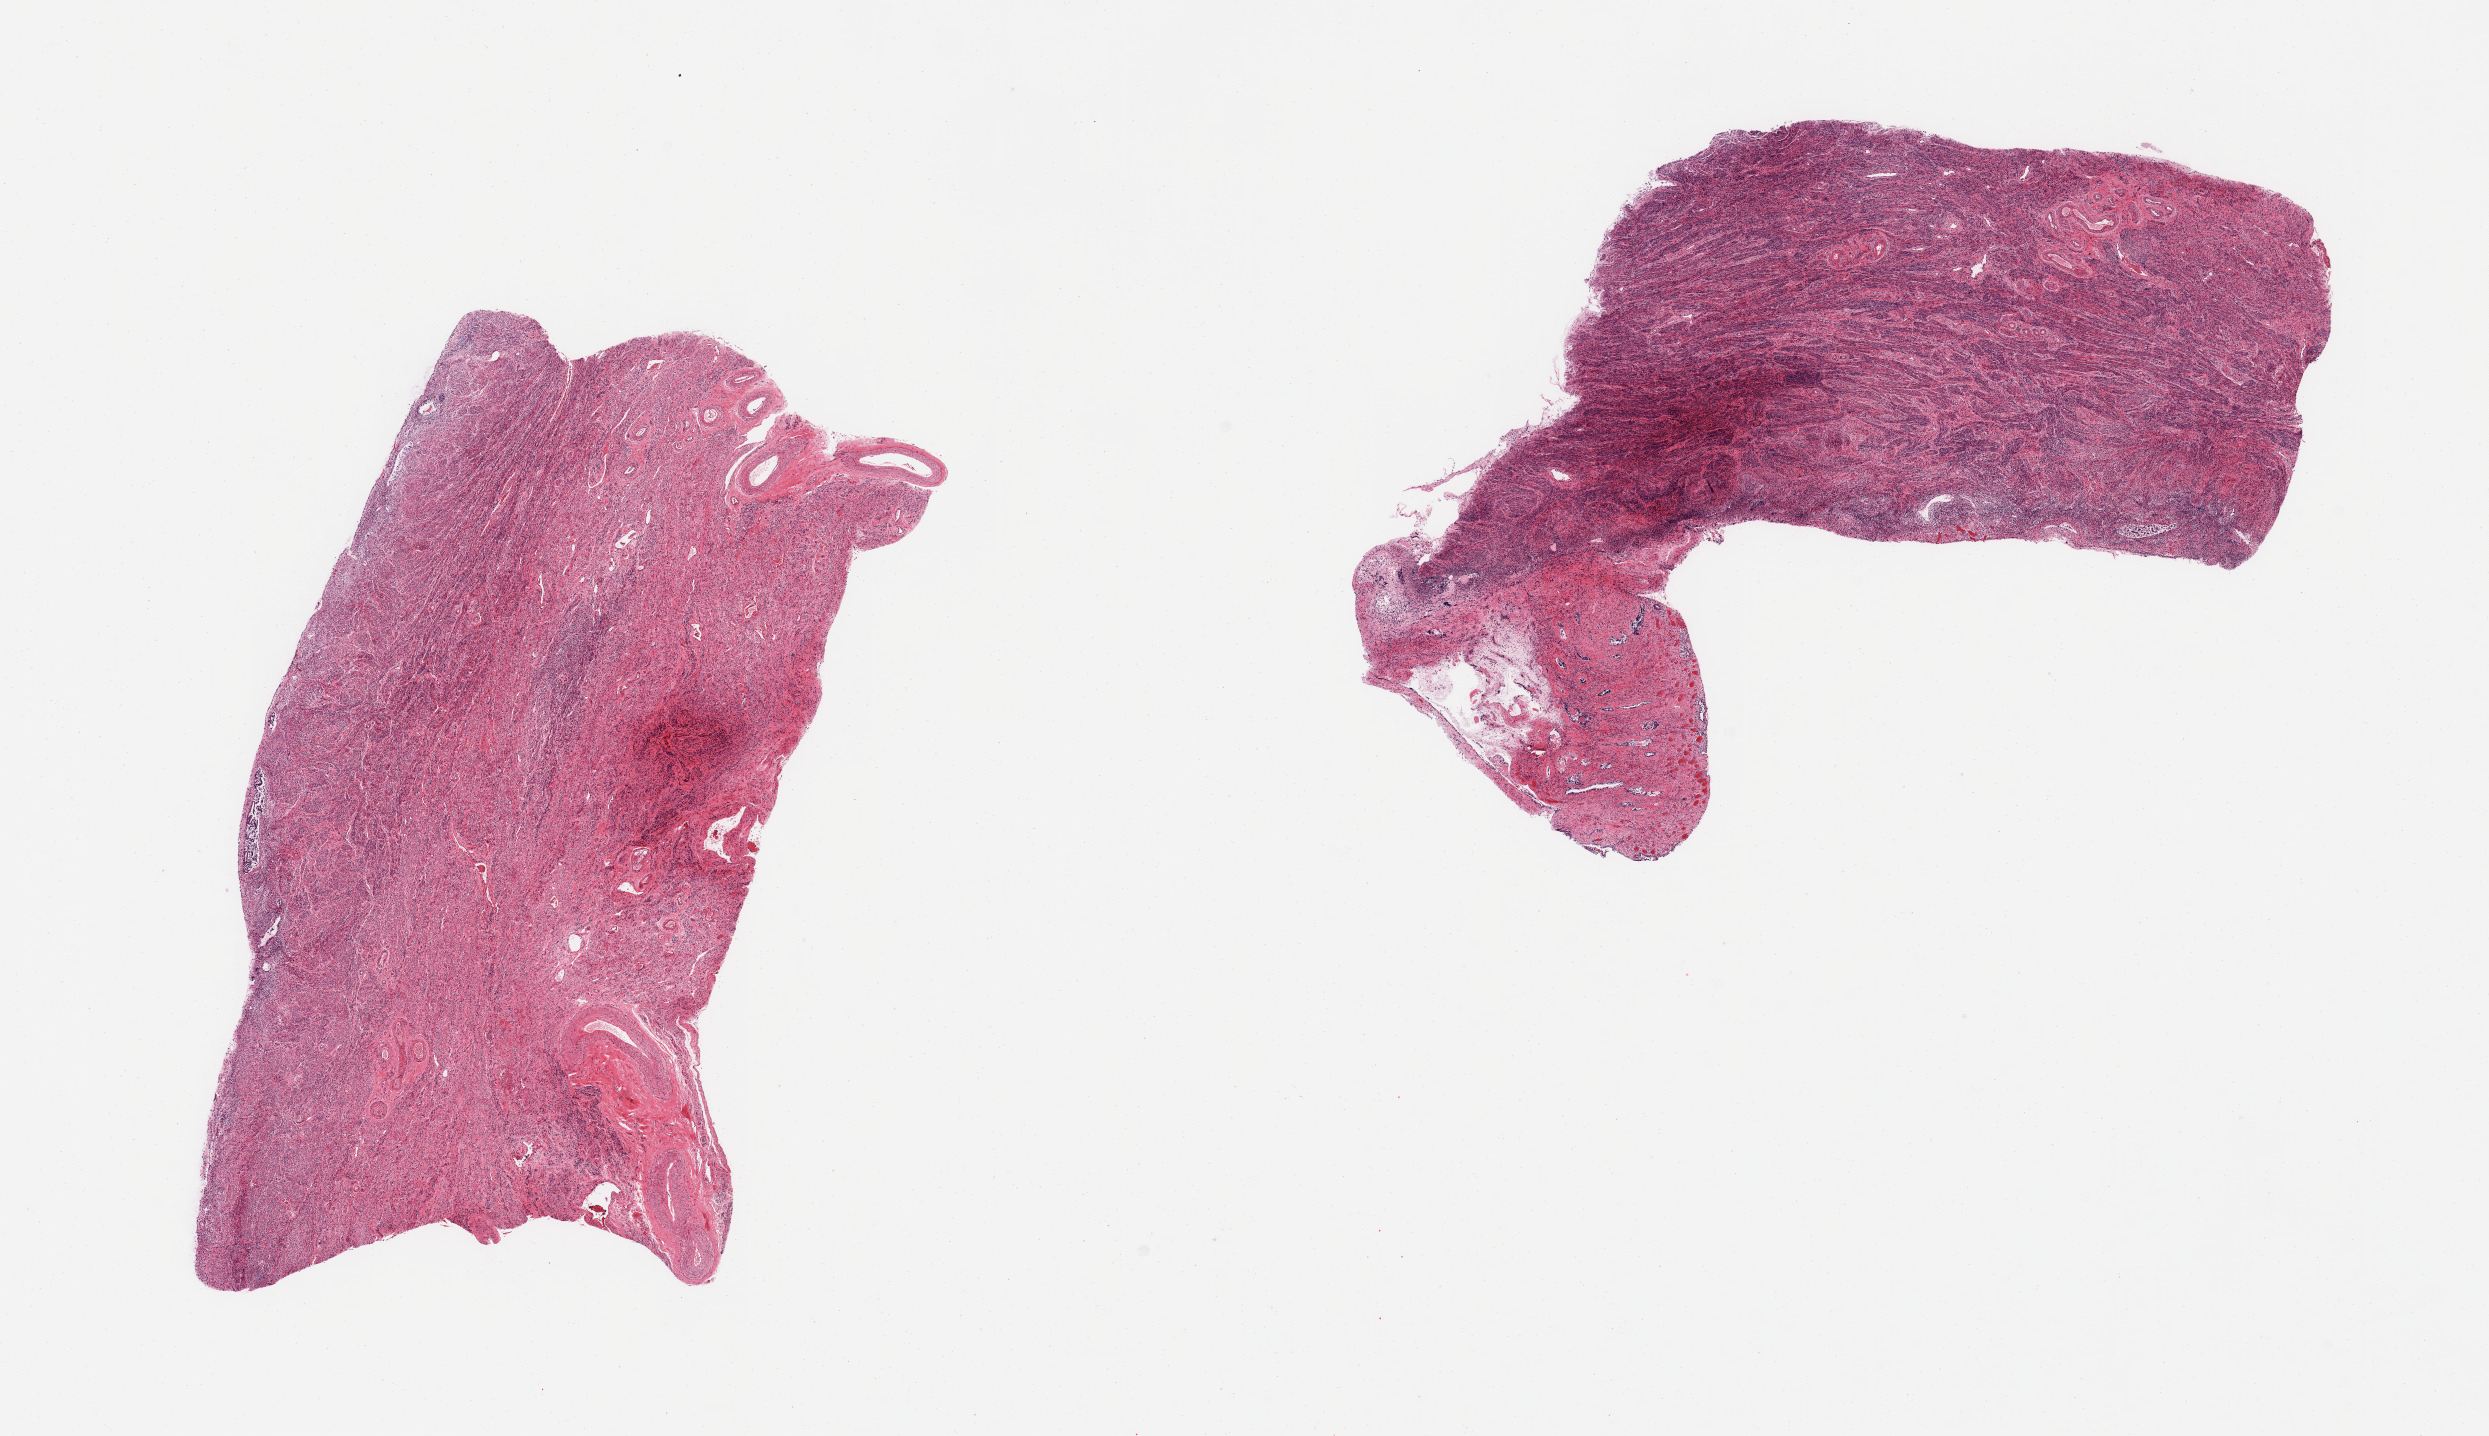
Digitized haematoxylin and eosin-stained section, low-resolution overview of the scanned area, about 19.7 x 11.4 mm (slide scanned at 20x); PAXgene-fixed, paraffin-embedded tissue; sampled site (target tissue): uterus; donor tissue sample.
- review note (as recorded): 2 pieces; glands in a portion of 1 piece are autolyzed and resemble cervical canal, not endometrium; adjacent endometrial glands and those in the other piece are autolyzed; stroma intact